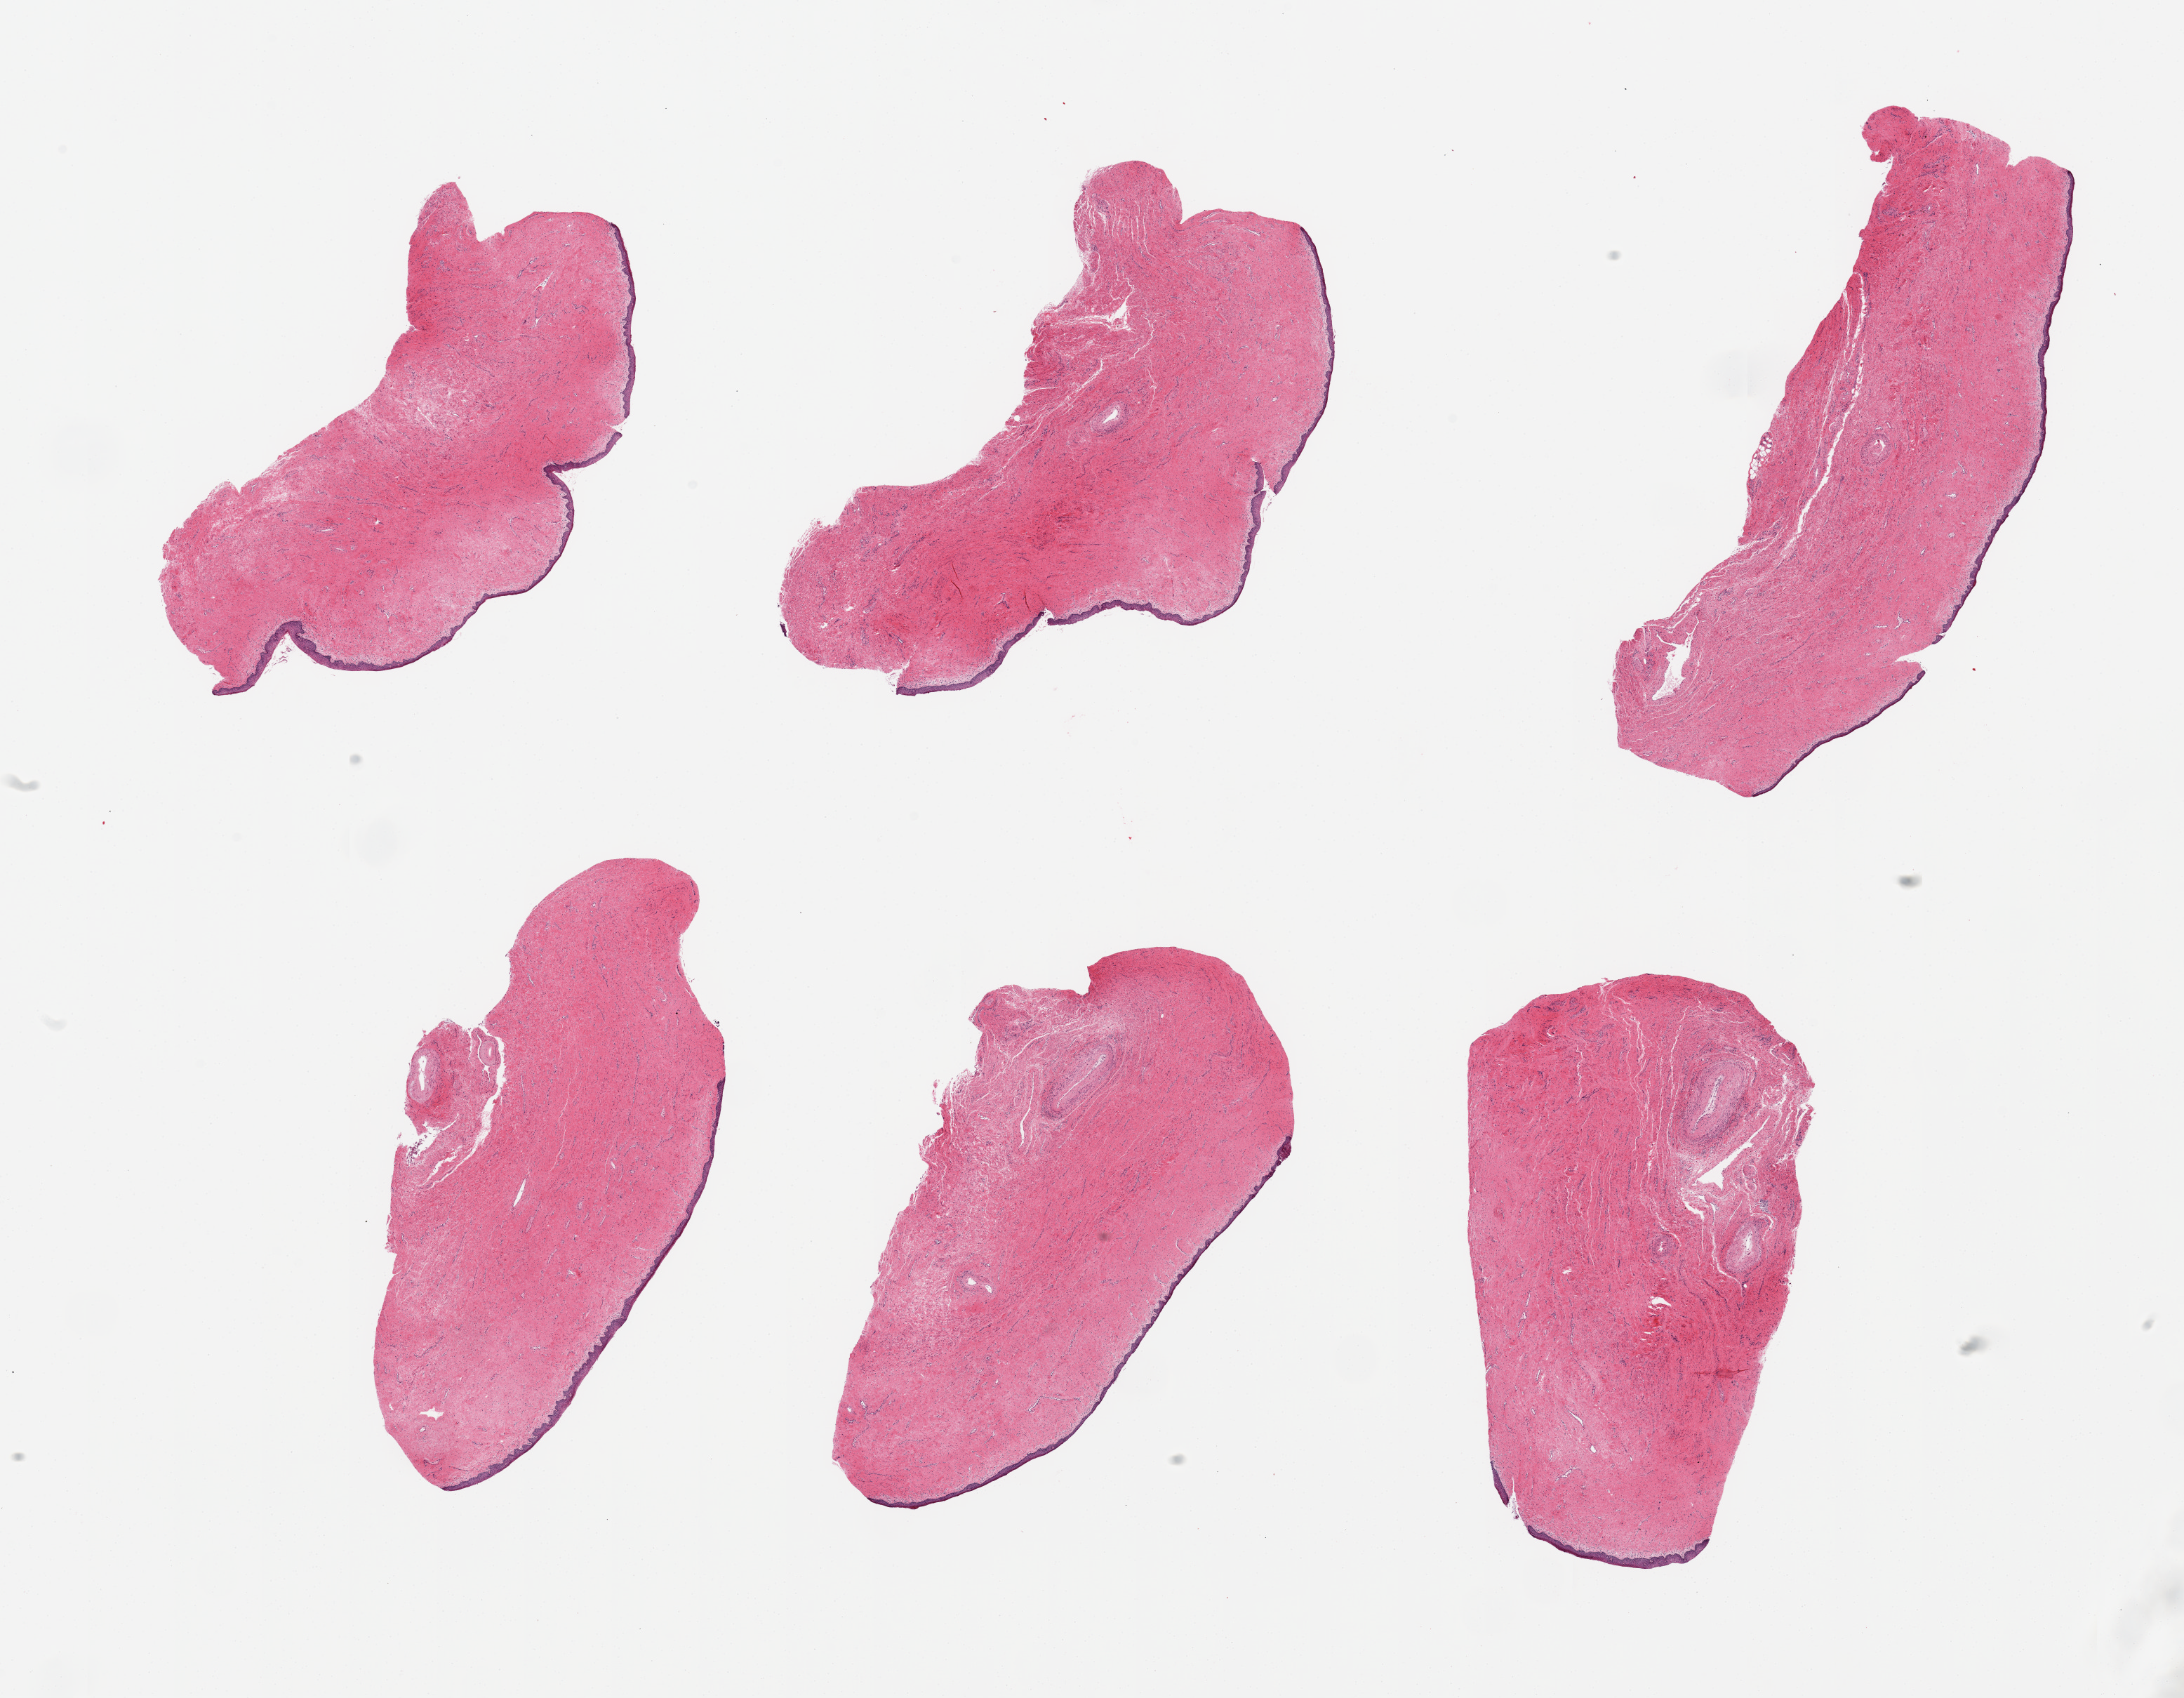
Whole-slide image, haematoxylin and eosin stain — a low-resolution overview of the entire scanned area, about 24.6 x 19.1 mm (acquisition: 20x scan); PAXgene-fixed paraffin-embedded (PFPE) section; target tissue: vagina; donor tissue sample. Donor: female.
Pathologist's review note for this sample: 6 pieces, squamous mucosa is ~75 microns, minimal adherent fat.